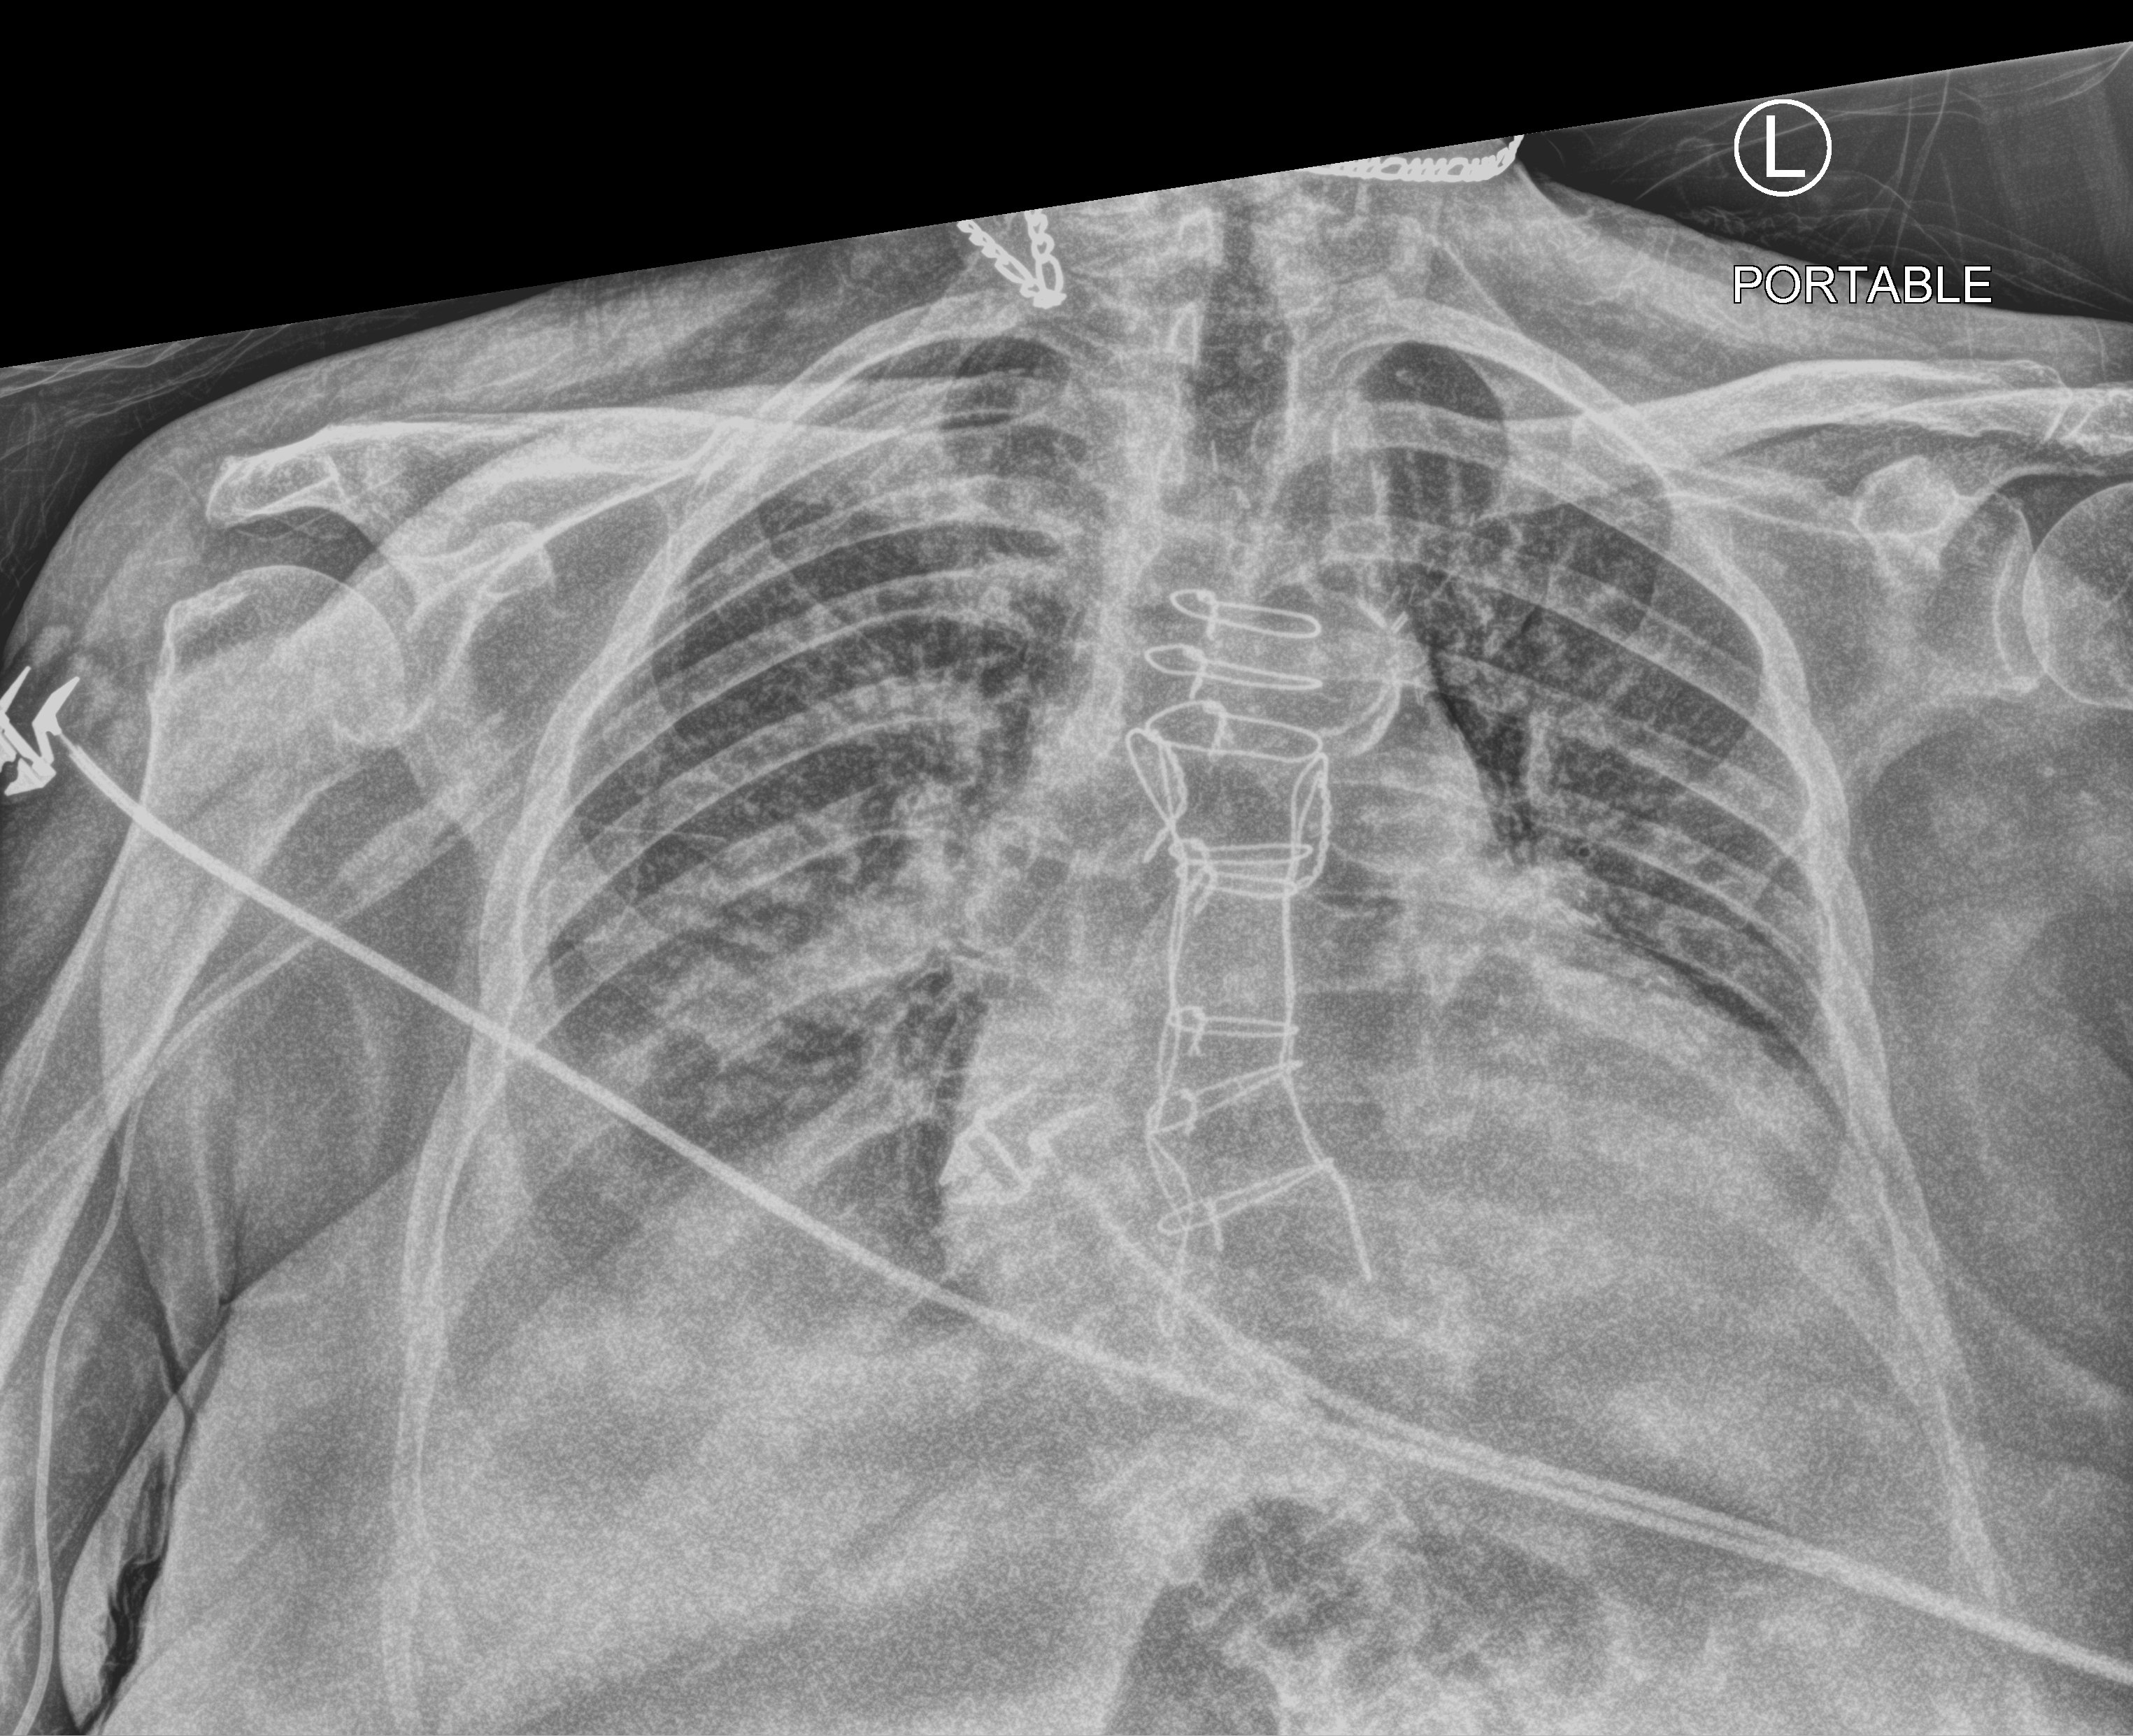
Bedside chest radiograph (computed radiography), anteroposterior (AP) projection. Female patient hospitalised with COVID-19, age 75–90 years.
From the hospital-stay record, not from the radiograph (when in the stay this image was taken is not recorded): mechanically ventilated during this hospital stay: no.